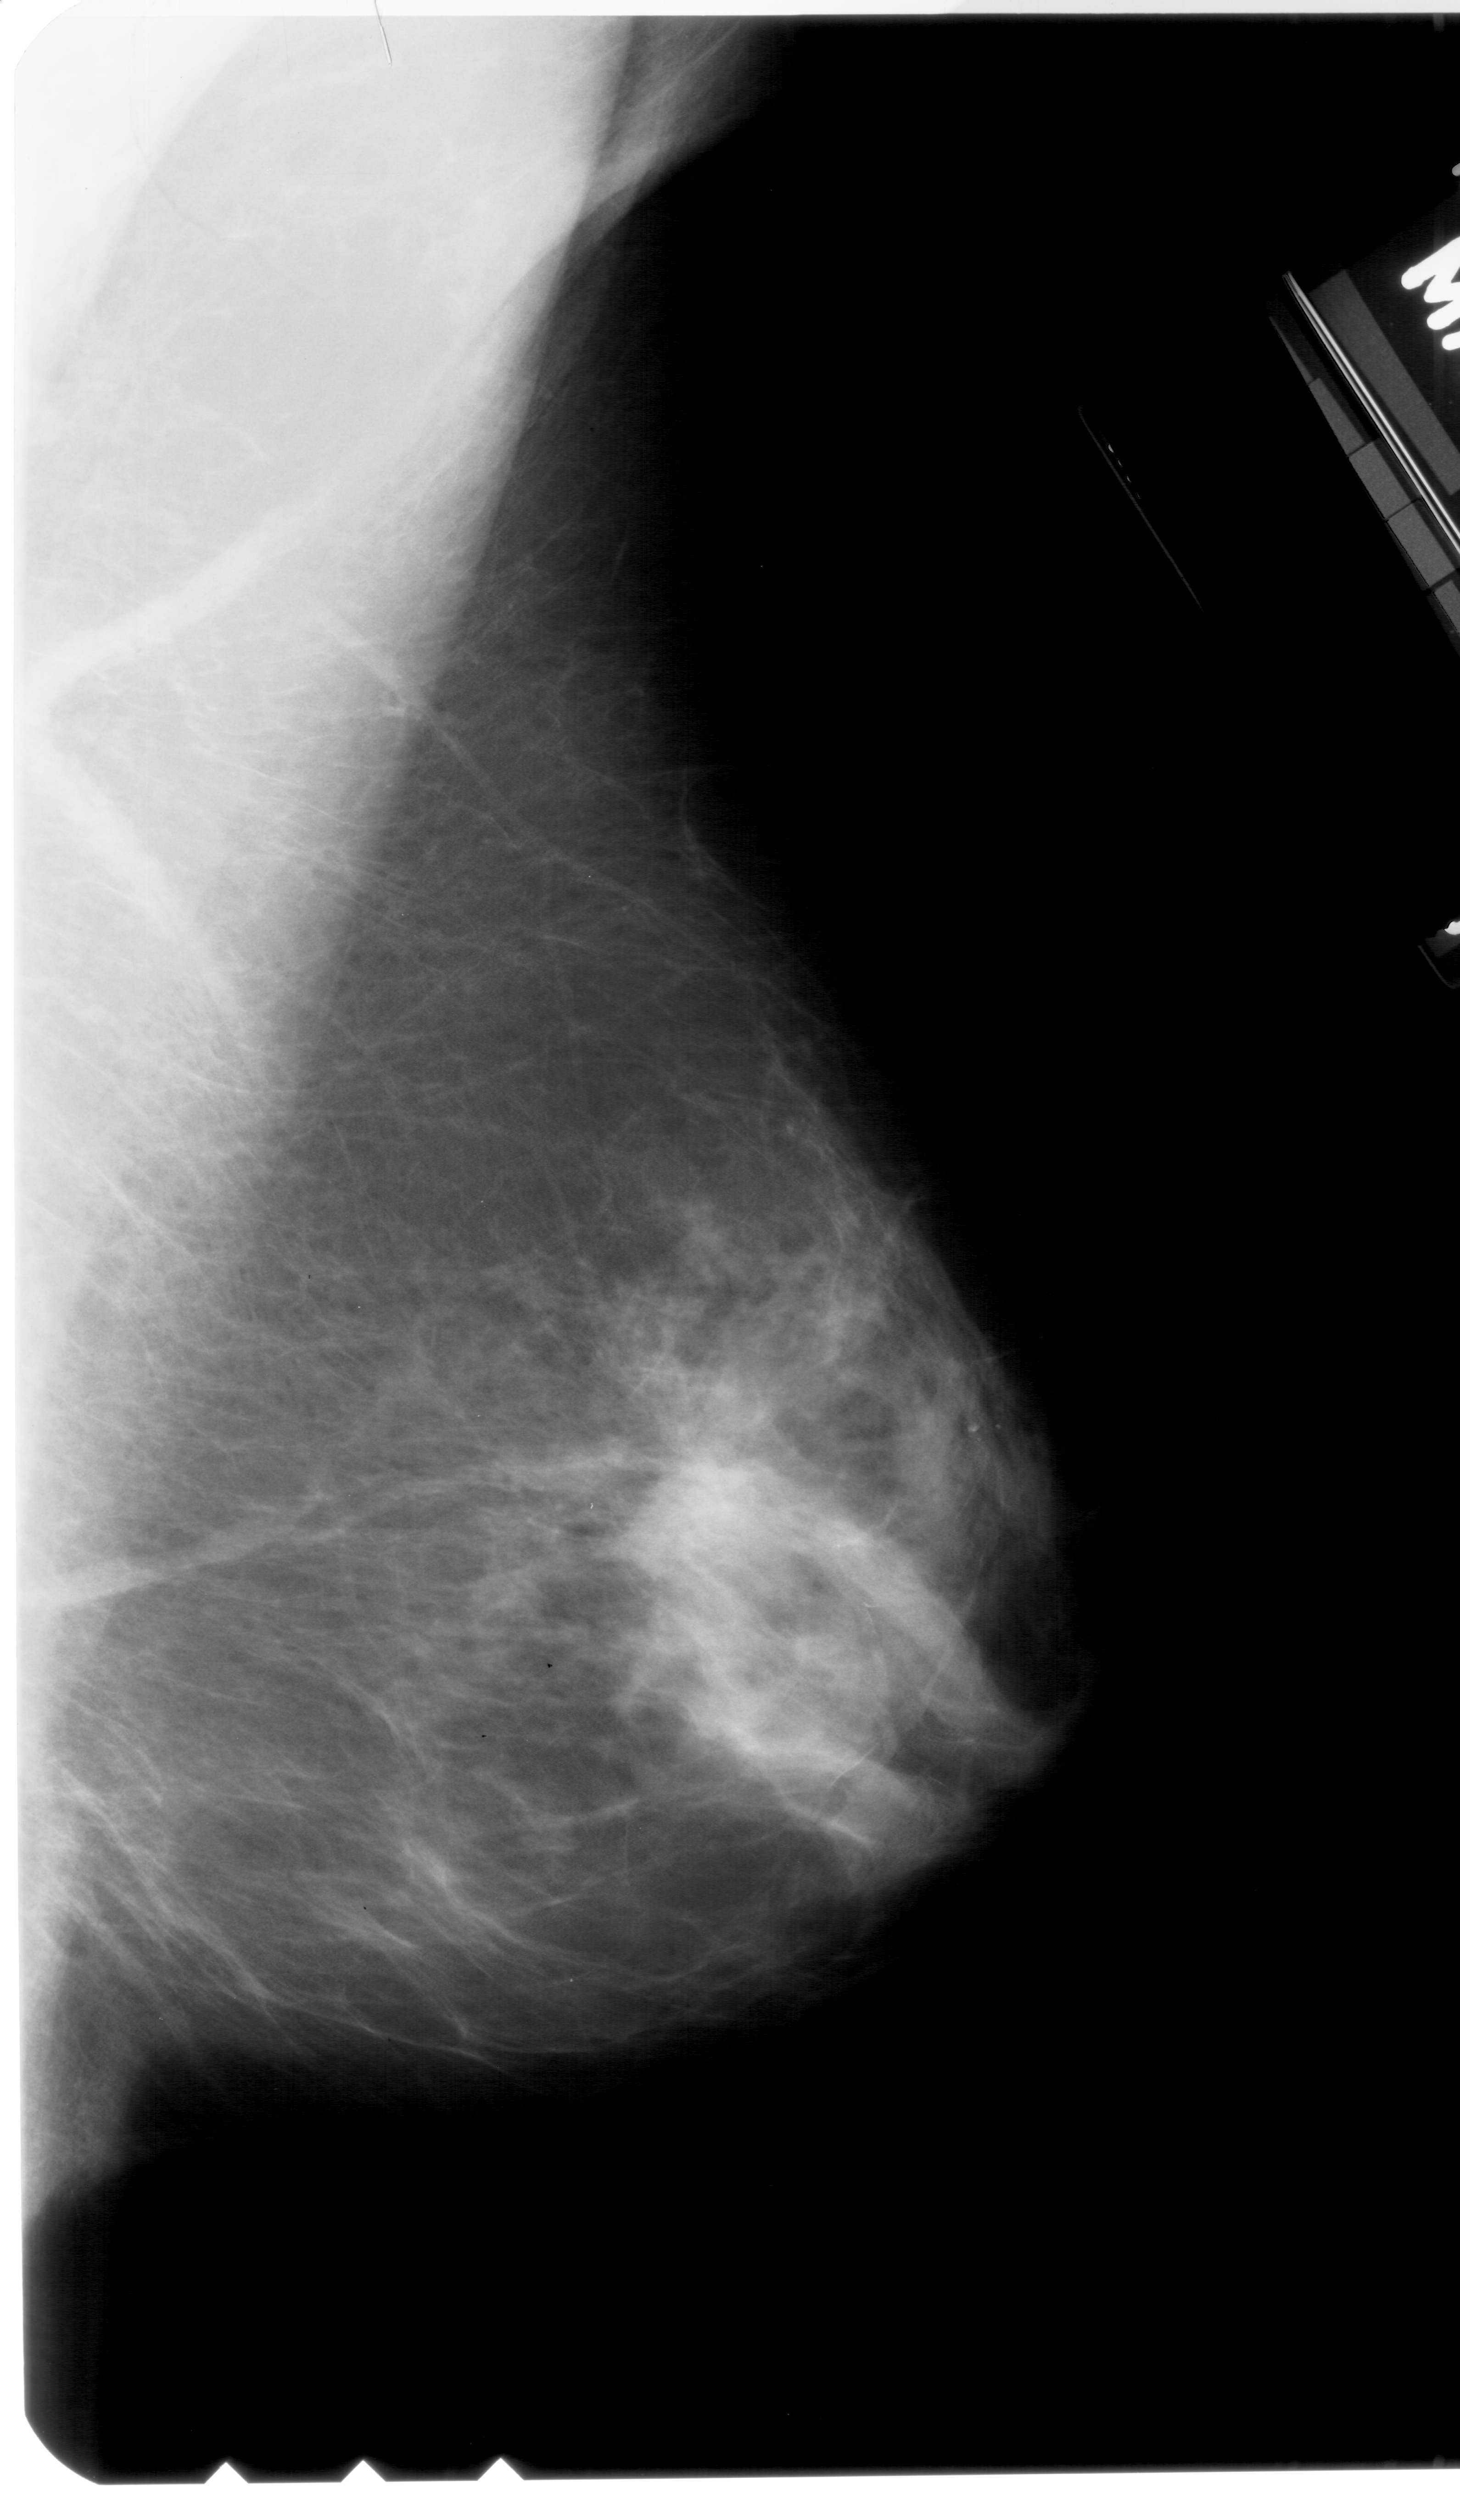
Scanned film-screen mammogram. Right breast. MLO view. BI-RADS breast density category 3 (scale 1–4). 1460 × 2520 image matrix.
Expert-marked regions of interest on this film, with their recorded descriptors:
- mass, shape irregular, margins ill defined; BI-RADS assessment category 4; subtlety rating 3 on a 1 (subtle) to 5 (obvious) scale; pathology result (as recorded, not read from the image): malignant: box from (x=637, y=1439) to (x=786, y=1569) px